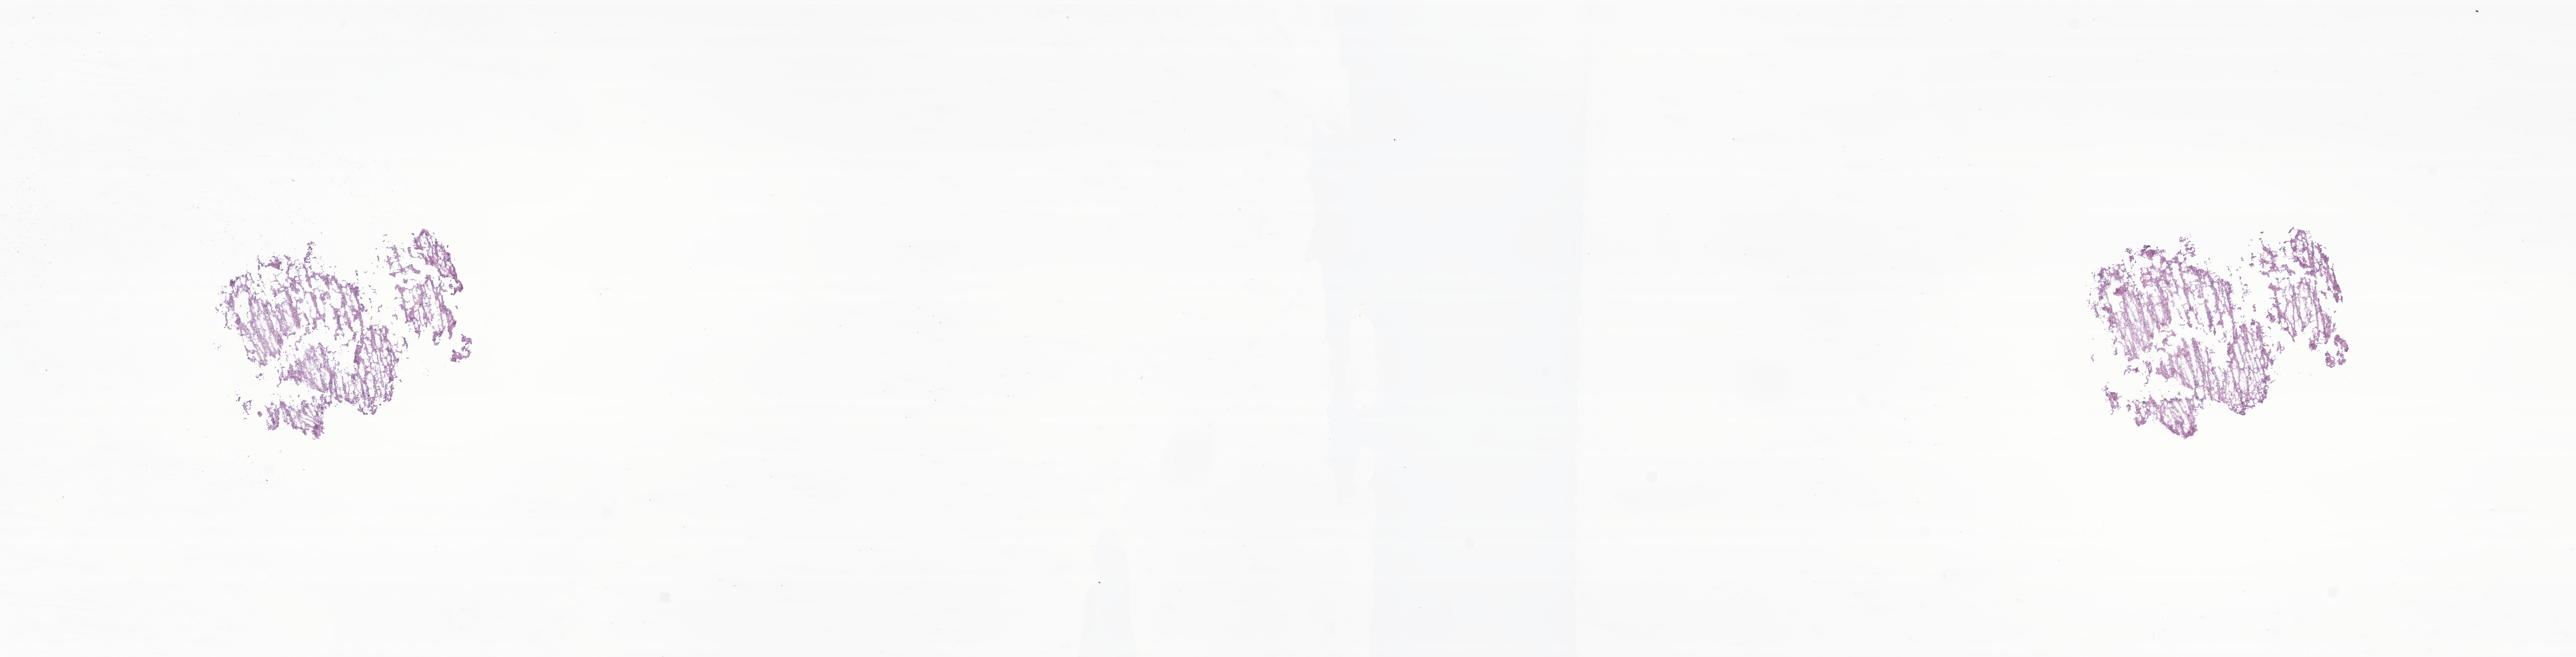
Whole-slide image, haematoxylin and eosin stain of tumor tissue from the cerebellum — shown as a low-resolution overview of the whole scanned area (about 22.3 x 5.7 mm), frozen section (OCT-embedded). Male patient, age 493 days (about 1.3 years).
Diagnosis: Ependymoma, NOS.